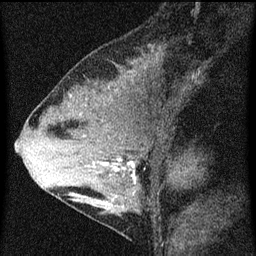
Breast MRI (dynamic contrast-enhanced), one sagittal slice; slice 31 of 60 in the series (ordered by position); dynamic contrast-enhanced series, image 2 of 3 at this slice position (ordered by acquisition); 1.5 T; TE 4.2 ms, TR 8 ms; 256 × 256 image matrix, field of view 180 × 180 mm. Patient: female, 33 years.
Annotated regions visible in this slice (semi-automatic segmentation, software-assisted and operator-edited):
- analysis volume of interest (the breast-tissue region the enhancement analysis was run in; not a lesion): bounding box (x1, y1, x2, y2) in pixels: (67, 118, 157, 215)
- tumour enhancement mask (voxels above the 70 % enhancement threshold inside the analysis volume of interest): (101, 158, 136, 197)